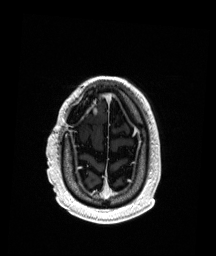
Brain MRI from a brain-tumour surgery series, one axial slice; position 35 of 192 along the scan axis; T1-weighted post-contrast; 1 mm slice thickness; 216 × 256 image matrix, field of view 211 × 250 mm. From the clinical record (not read from this slice): histopathology: Astrocytoma; WHO grade: 3; IDH mutation: yes.
Structures marked on this image (manually delineated by an expert):
- previous resection cavity: box from (x=90, y=110) to (x=93, y=114) px